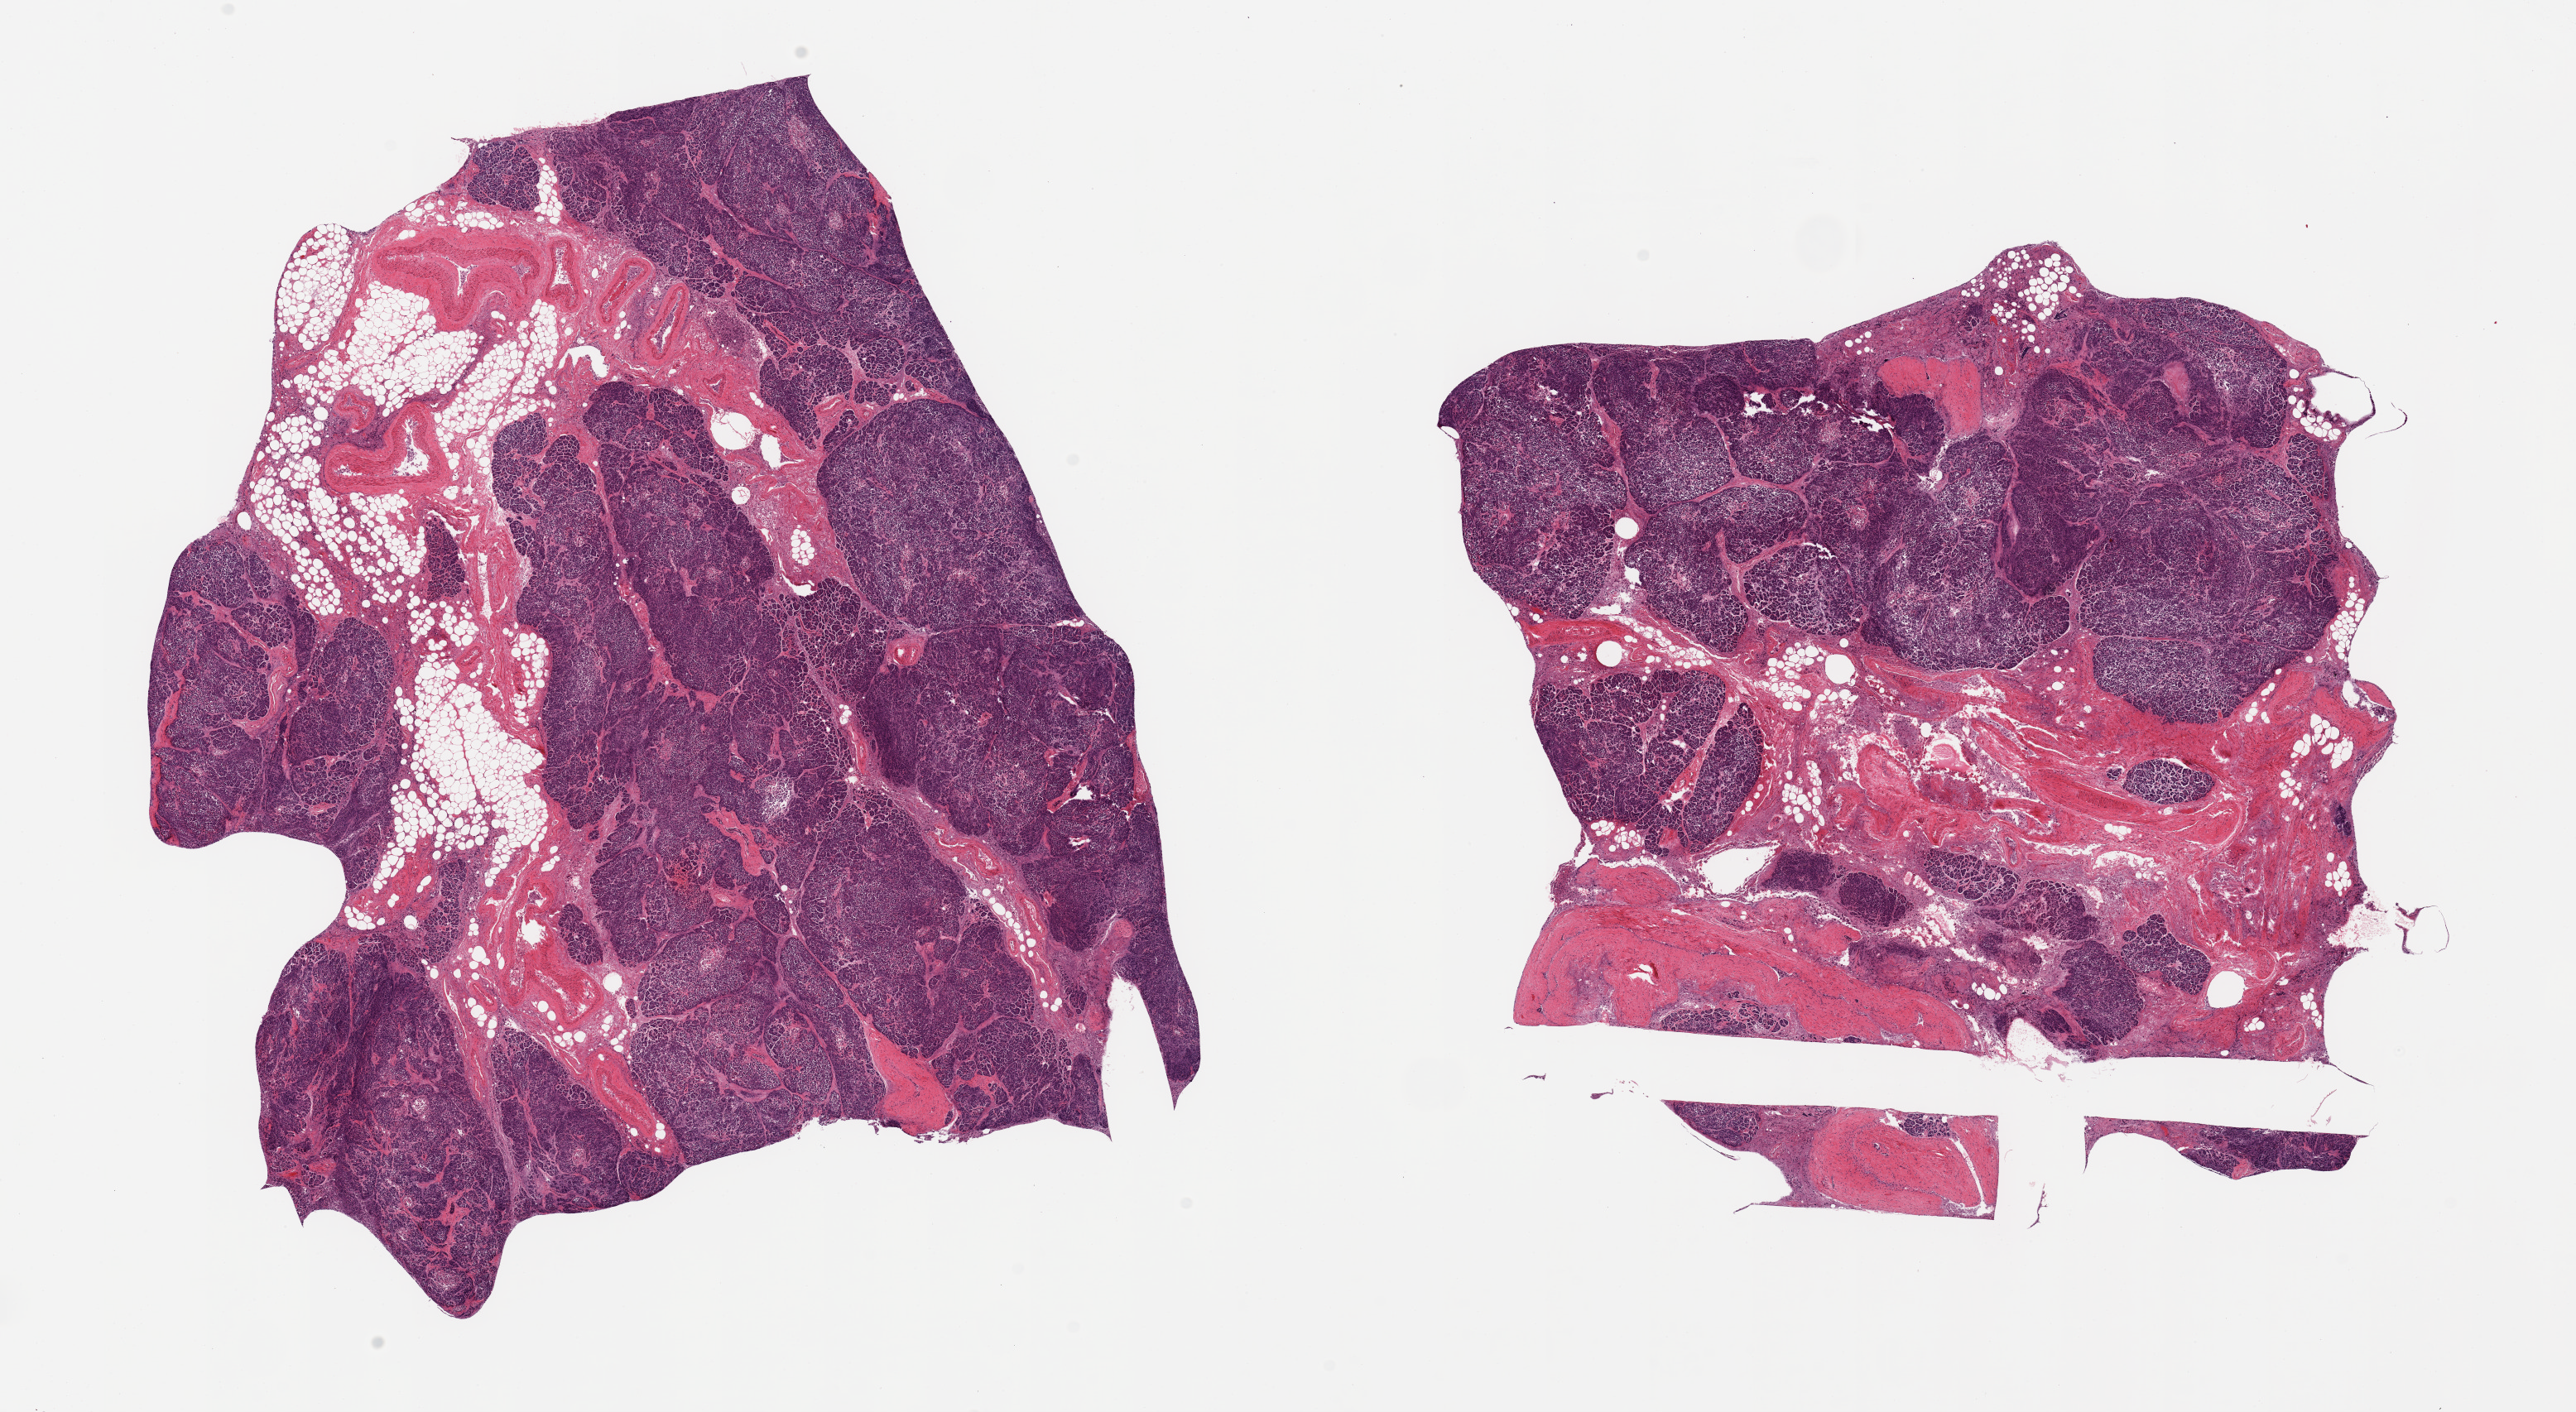
Whole-slide image, H&E stain — shown as a low-resolution overview of the whole scanned area (about 24.6 x 13.5 mm, slide scanned at 20x); PAXgene-fixed paraffin-embedded (PFPE) section; sampled site (target tissue): pancreas; tissue donor sample. Donor sex: male.
Reviewer comment on this tissue sample: 2 pieces; up to 40% fat /large vessels, moderate to severe autolysis, some fibrosis.